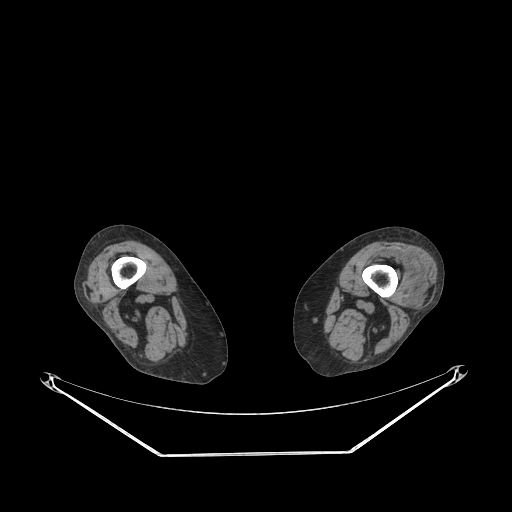
CT of an extremity soft-tissue mass (from a PET/CT study), one axial slice. Soft-tissue window (W 400 / L 40 HU). 512 × 512 image matrix, field of view 500 × 500 mm. Female patient. Case-level facts recorded for this patient, not image findings: histological type: undifferentiated – high grade; grade: high; site of the primary tumour: left thigh.
Annotated regions visible in this slice (expert contour drawn on MRI and transferred to this co-registered scan by the dataset authors):
- gross tumour volume including surrounding oedema: bounding box <386,253,423,296> (left, top, right, bottom; pixels)